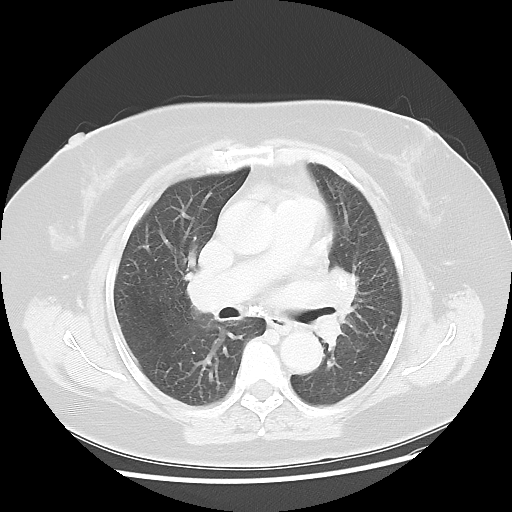
Chest CT, one axial slice. Slice 26 of 49 in the series (ordered by position). 120 kVp. Lung window (W 1500 / L -600 HU). 5 mm slice thickness. 512 × 512 image matrix, field of view 374 × 374 mm. Patient: female, 58 years. Case-level facts recorded for this patient, not image findings: clinical TNM (as recorded): T4 N3 M0.
Outlined on this slice (bounding box drawn by a radiologist):
- lung tumour (recorded histology: small cell carcinoma): box from (x=313, y=259) to (x=358, y=364) px